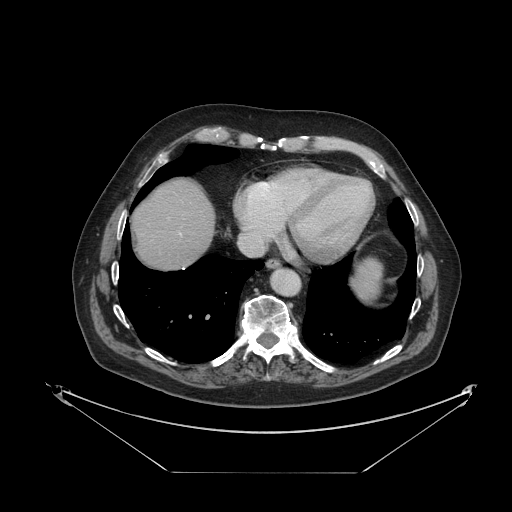
Contrast-enhanced abdominal CT, one axial slice. Slice 113 of 121 in the series (ordered by position). Reconstruction kernel STANDARD. Soft-tissue window (W 400 / L 40 HU). 2.5 mm slice thickness. 512 × 512 image matrix, field of view 500 × 500 mm. Male patient, age 68 years. Case-level facts recorded for this patient, not image findings: diagnosis: colorectal cancer liver metastases, imaged before liver resection; multiple liver metastases: no; largest metastasis: 4 cm; disease in both lobes: no.
Annotated regions visible in this slice (expert manual segmentation):
- liver: bounding box [x1, y1, x2, y2] px = [134, 180, 215, 269]
- planned liver remnant (the part of the liver to remain after resection): [134, 181, 215, 269]